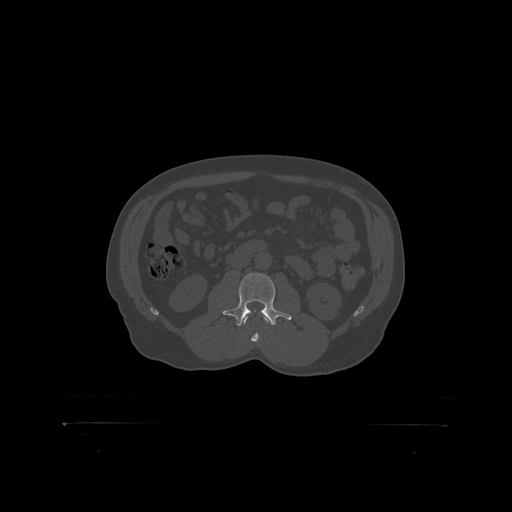
CT including the spine, one axial slice. Slice 273 of 399 in the series (ordered by position). Reconstruction kernel STANDARD. Bone window (W 1800 / L 400 HU). 1.25 mm slice thickness. 512 × 512 image matrix, field of view 650 × 650 mm. Patient: male, 46 years. From the clinical record (not read from this slice): primary cancer: skin.
Outlined on this slice (semi-automatically segmented with operator editing):
- L2 vertebra: bounding box (x1, y1, x2, y2) in pixels: (244, 316, 249, 319)
- L3 vertebra: (227, 273, 282, 319)